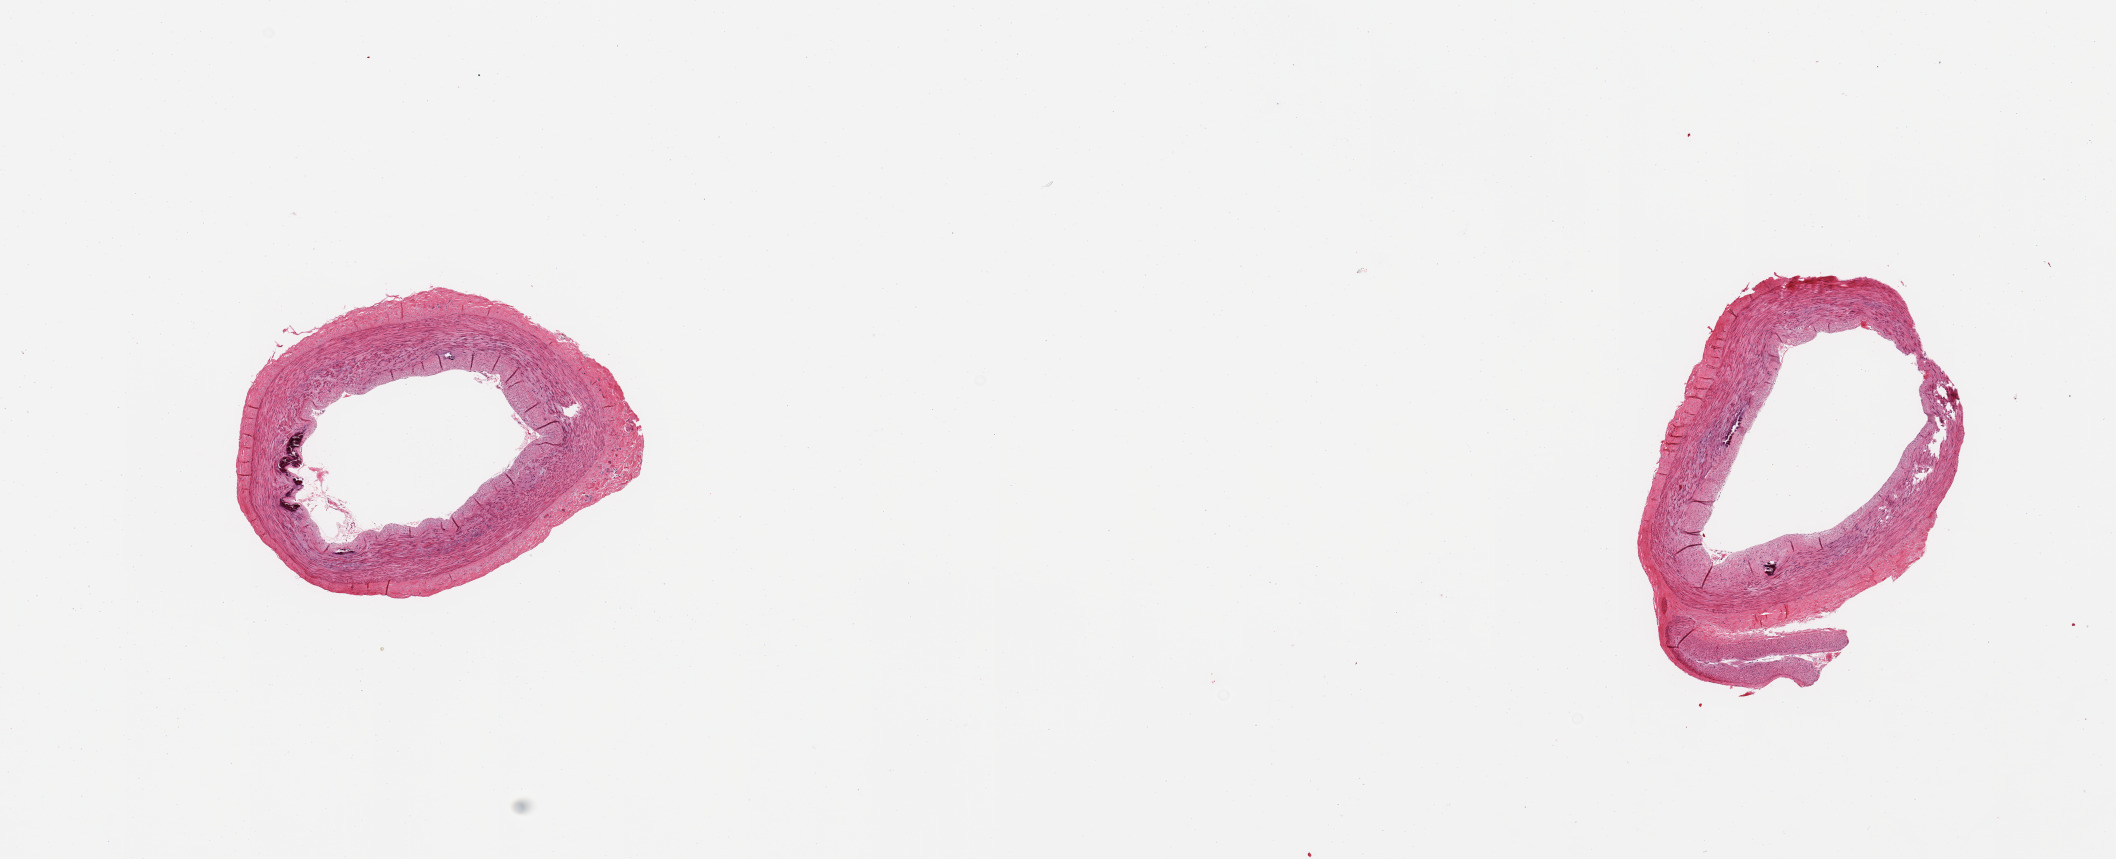
H&E whole-slide image, low-resolution overview of the scanned area, about 16.7 x 6.8 mm (slide scanned at 20x); PAXgene-fixed, paraffin-embedded tissue; section of tibial artery (target tissue); tissue donor sample. Donor sex: male.
Reviewer comment on this tissue sample: 2 pieces; thin flat intimal plaques with focal calcifications.